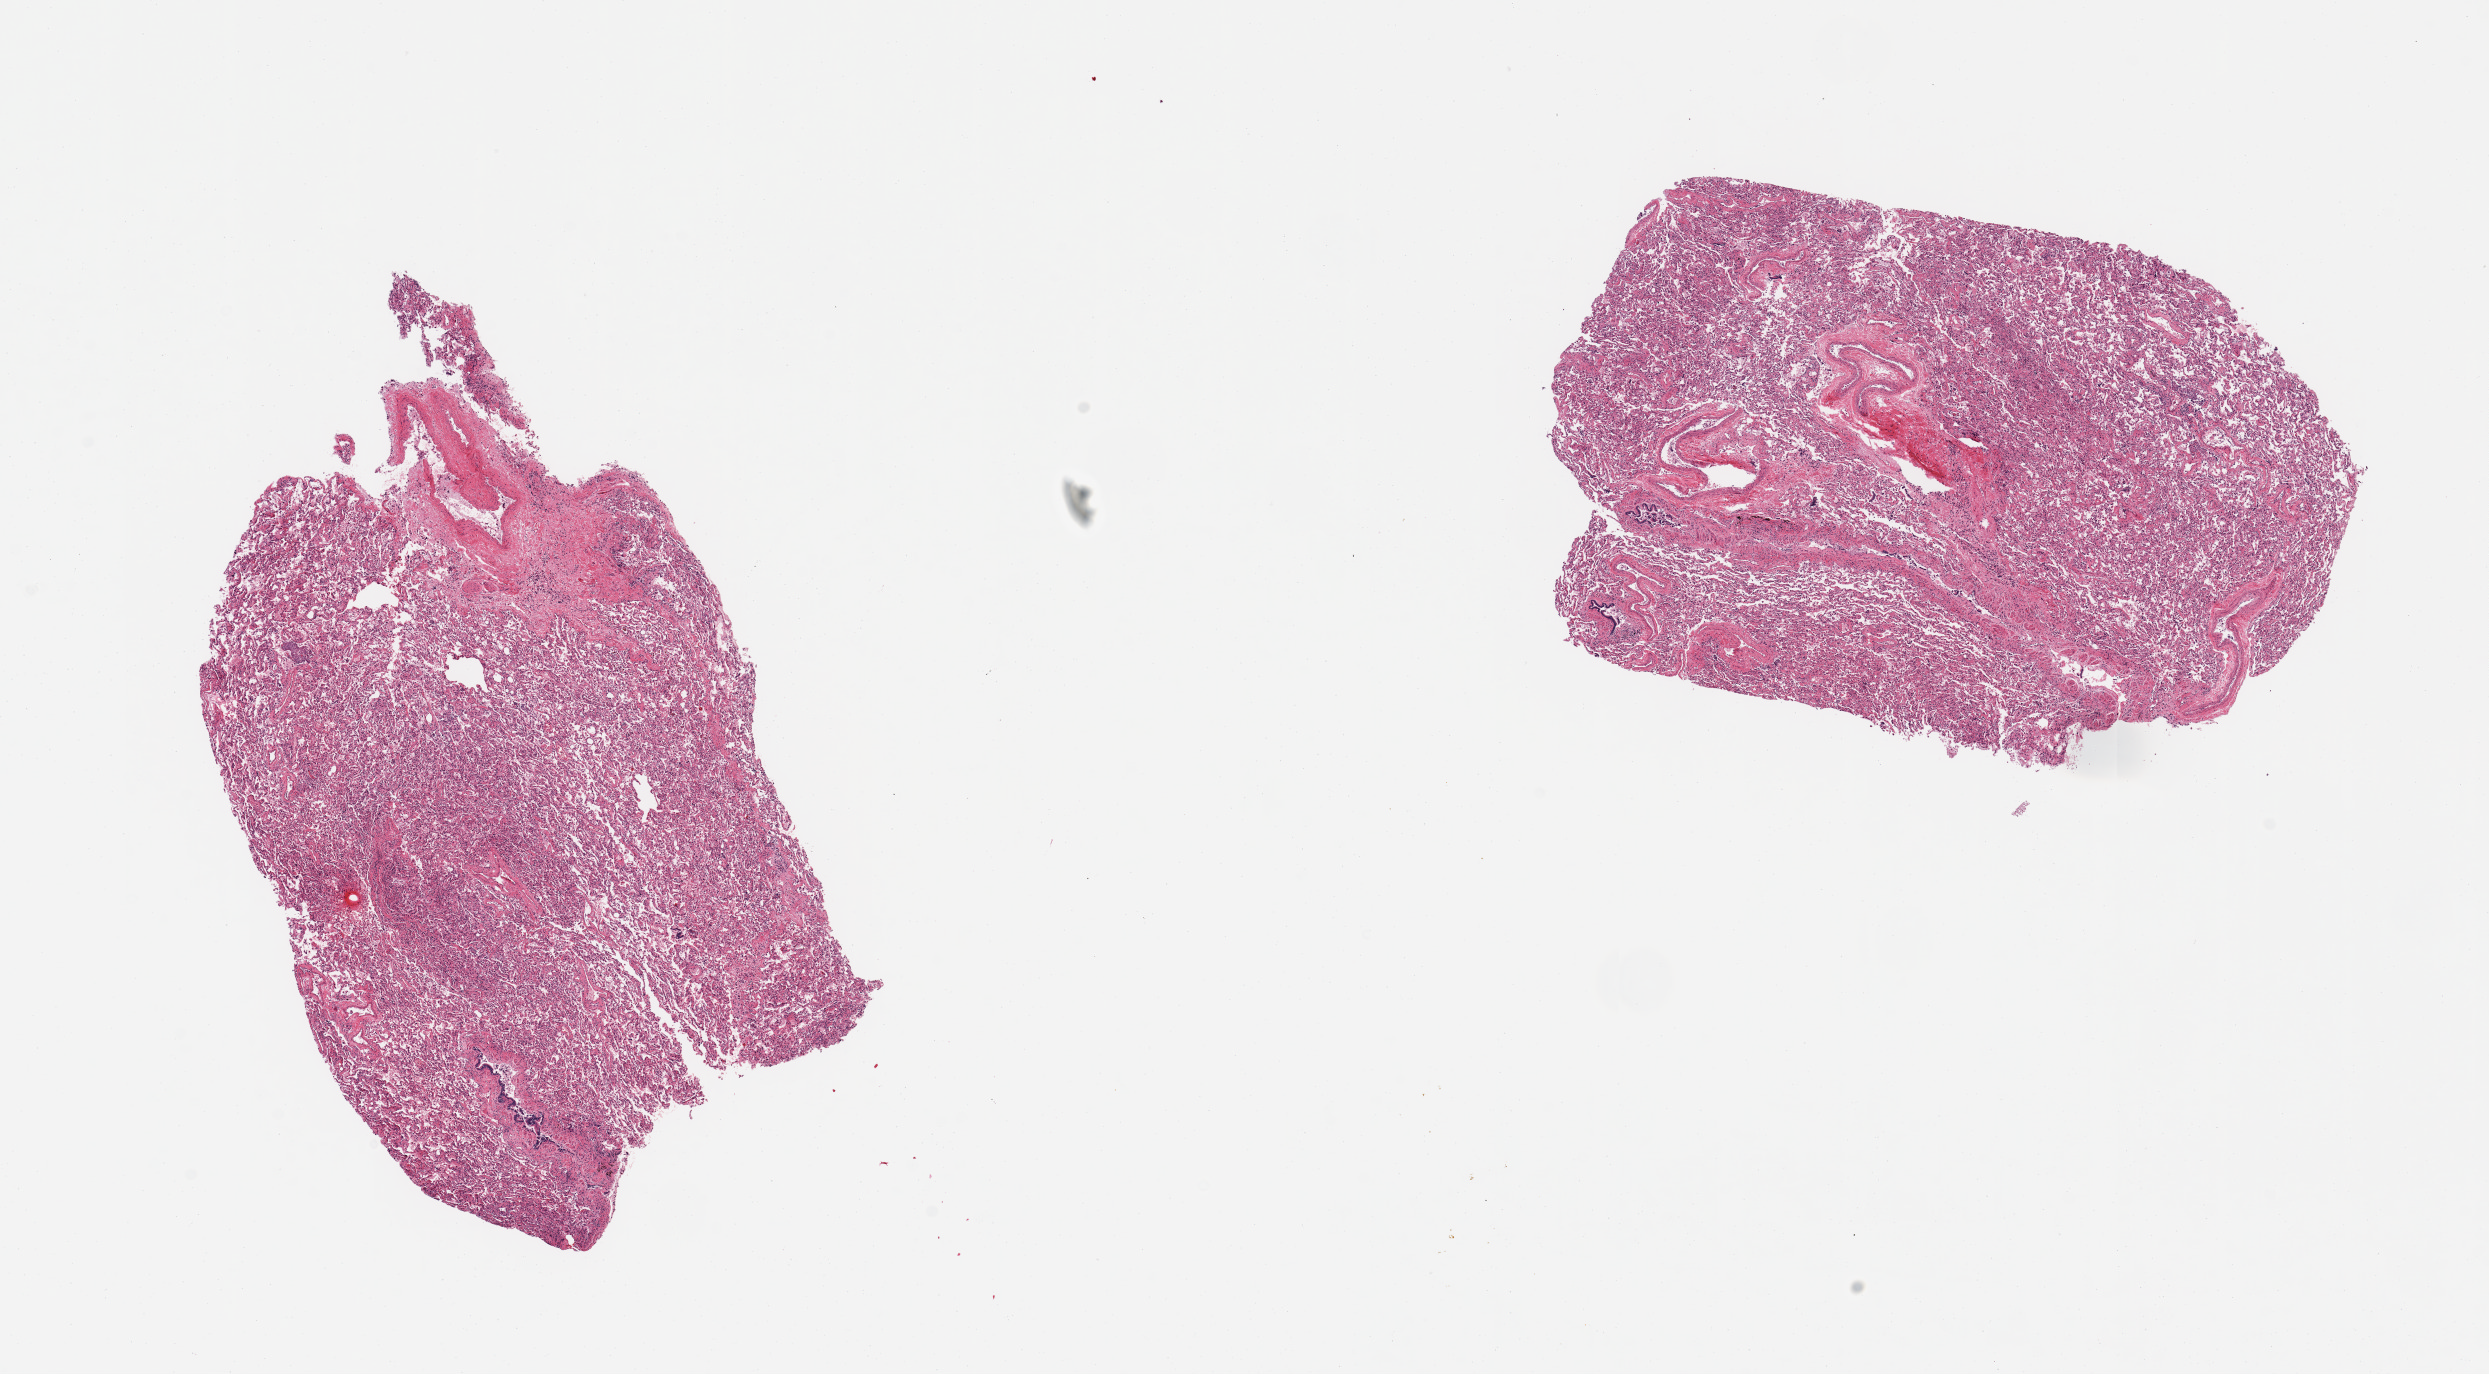
Digitized H&E-stained section, shown as a low-resolution overview of the whole scanned area (about 19.7 x 10.9 mm). PAXgene-fixed, paraffin-embedded tissue. Section of lung (target tissue). Donor tissue sample. Donor: male.
Review note (as recorded): 2 pieces; congestion and collapsed alveolar spaces containing exfoliated alveolar epithelial cells; larger vessels included.